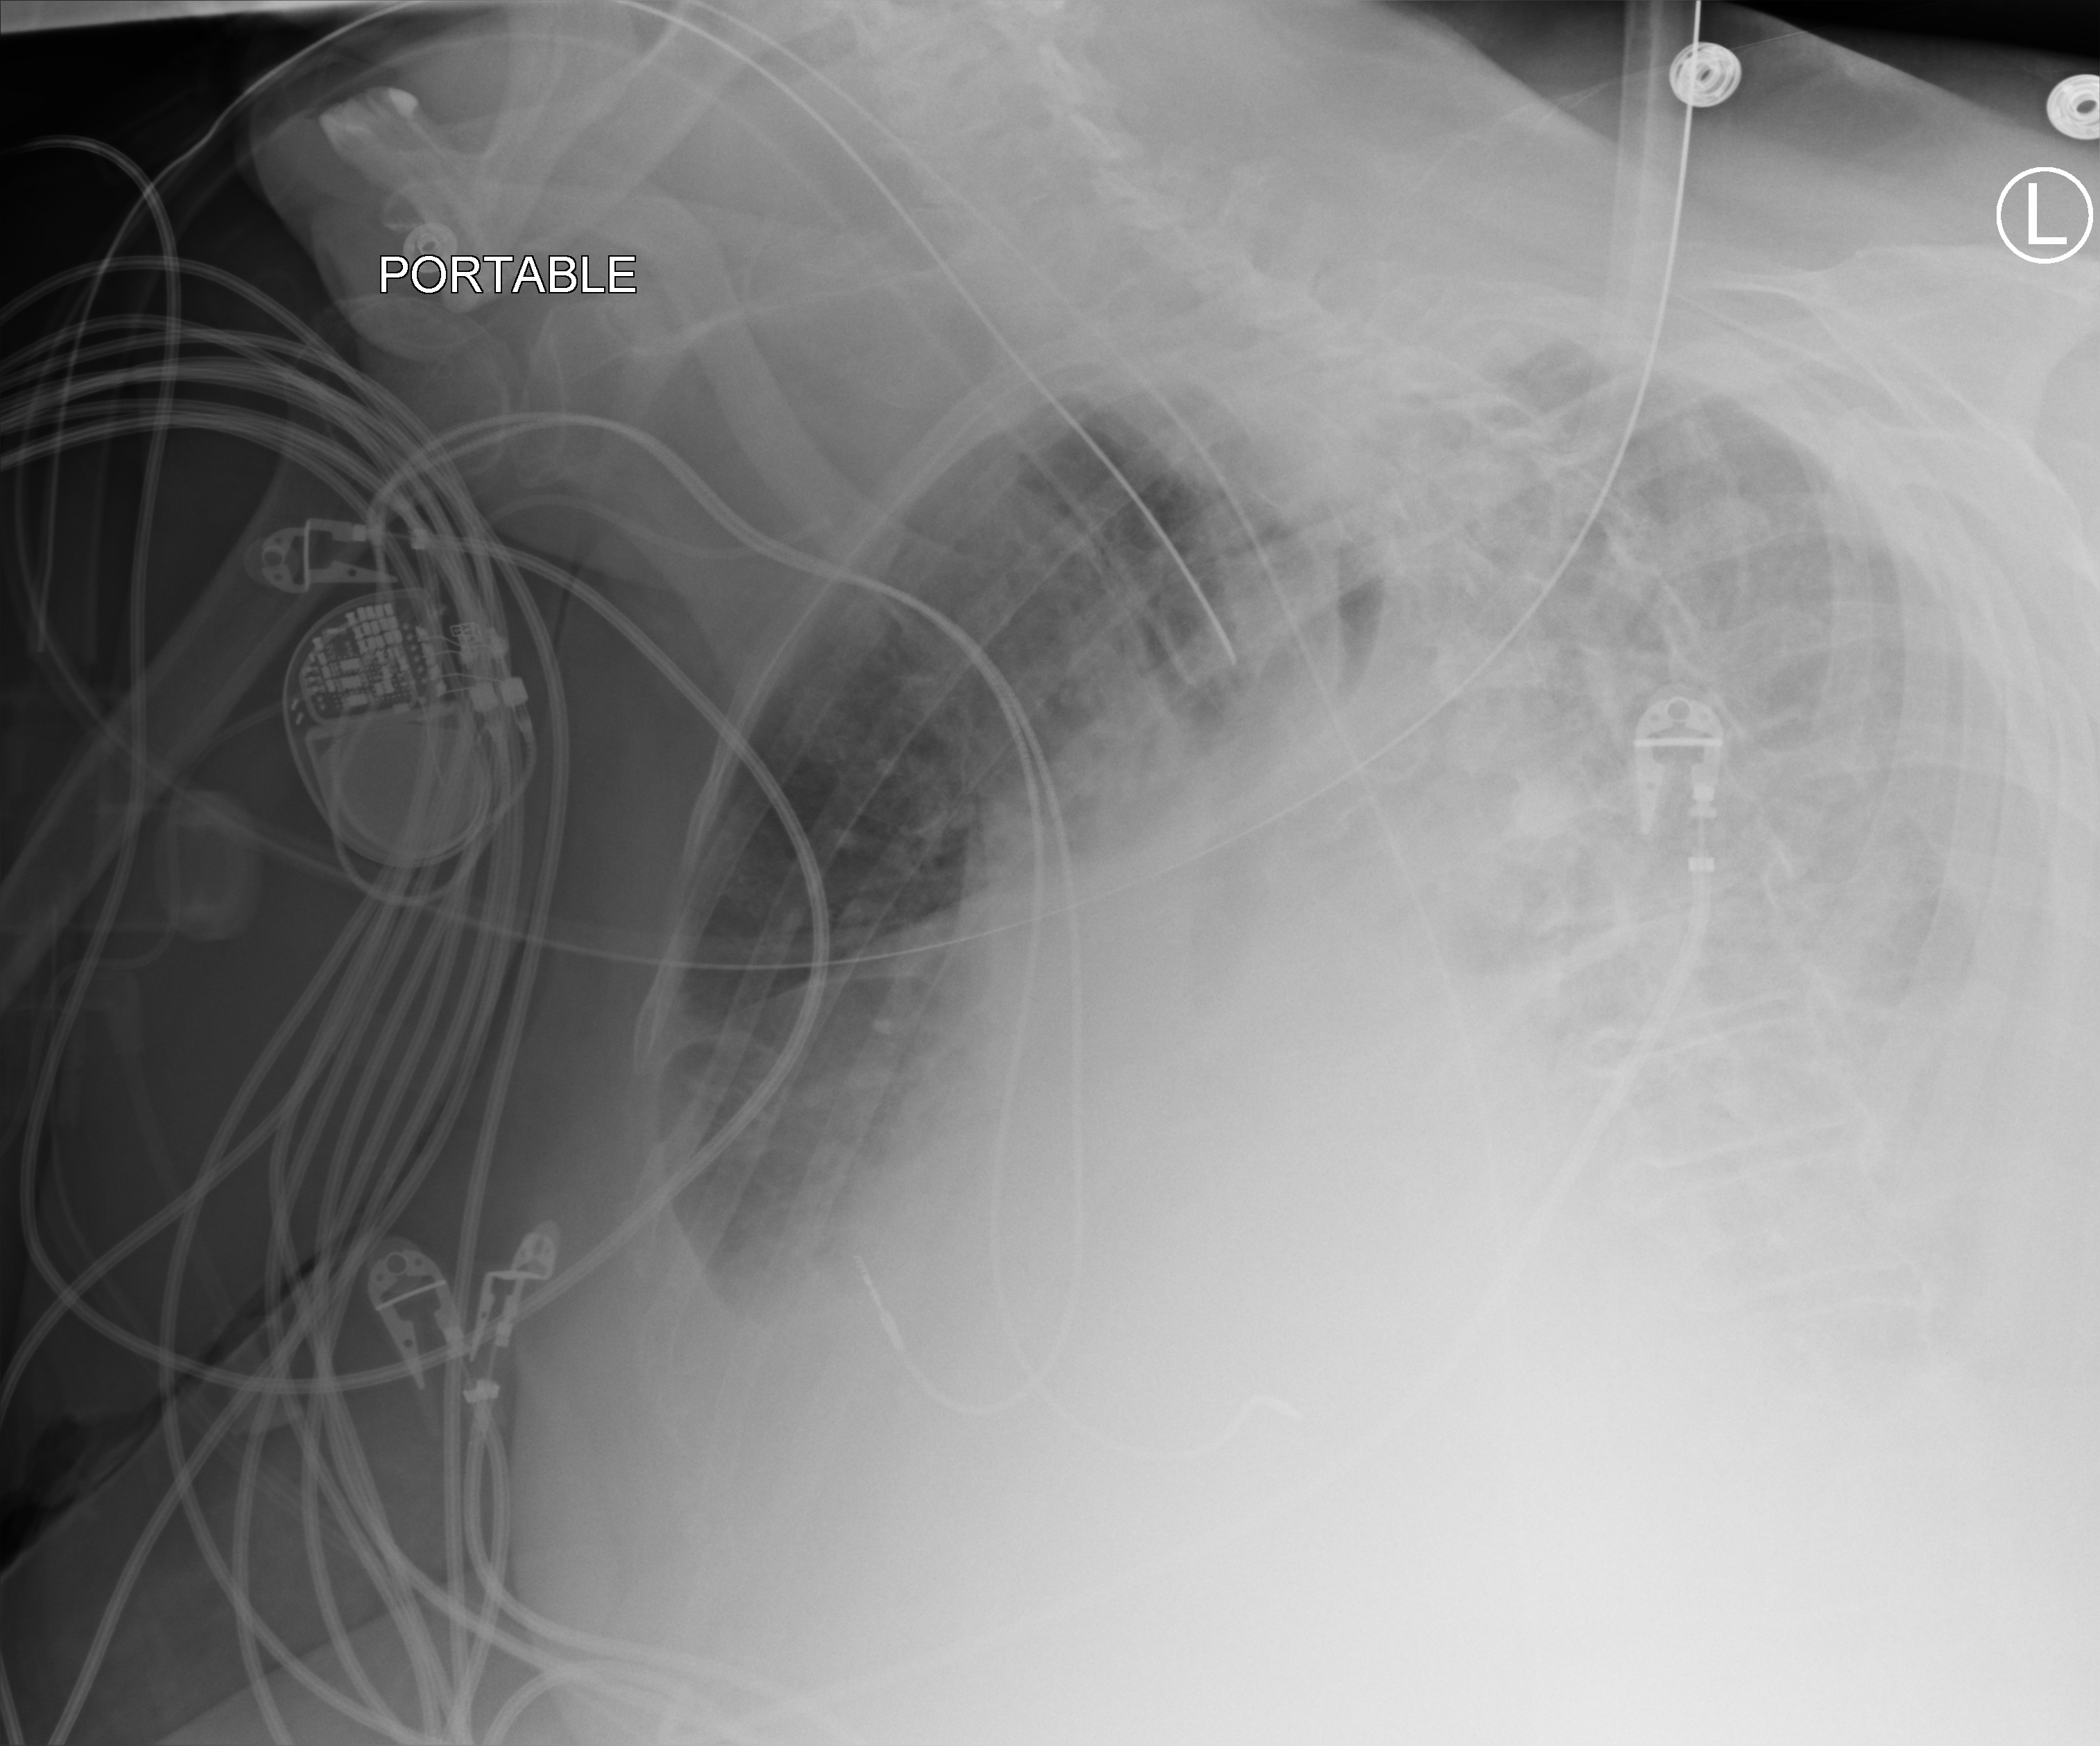
Chest X-ray (portable); anteroposterior (AP) projection. Patient hospitalised with COVID-19; female, aged 75–90 years.
Admission-level facts for this patient (not findings on this image; timing relative to this image not recorded): mechanically ventilated during this hospital stay: yes.